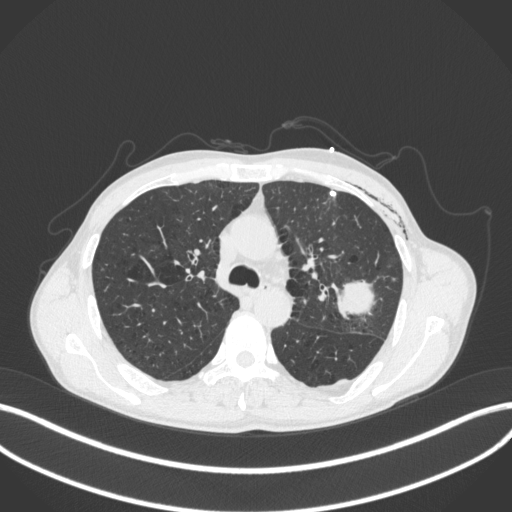
Chest CT, one axial slice. Position 270 of 416 along the scan axis. 120 kVp. Lung window (W 1500 / L -600 HU). 1 mm slice thickness. 512 × 512 image matrix. Male patient, age 58 years. From the clinical record (not read from this slice): clinical TNM (as recorded): T3 N0 M0.
Structures marked on this image (bounding box drawn by a radiologist):
- lung tumour (recorded histology: adenocarcinoma): bounding box (x1, y1, x2, y2) in pixels: (334, 275, 378, 323)